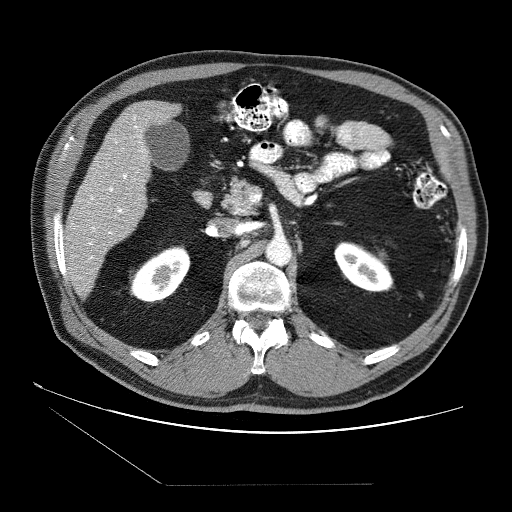
Contrast-enhanced abdominal CT (liver protocol), one axial slice. Slice 28 of 87 in the series (ordered by position). 120 kVp. Soft-tissue window (W 400 / L 40 HU). 2.5 mm slice thickness. 512 × 512 image matrix, field of view 400 × 400 mm. Case-level facts recorded for this patient, not image findings: diagnosis: hepatocellular carcinoma (patient treated with transarterial chemoembolisation; whether this scan precedes or follows treatment is not stated here); TNM stage (as recorded): Stage-II.
Structures marked on this image (semi-automatic segmentation, software-assisted and operator-edited):
- liver parenchyma outside the tumour (the mass and vessels are separate outlines, so this box may not span the whole liver): bounding box <66,100,180,286> (left, top, right, bottom; pixels)
- liver vessels: <80,115,146,278>